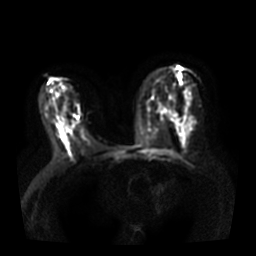
Breast MRI, one axial slice. Position 18 of 36 along the scan axis. Diffusion-weighted series; image 2 of 4 stored at this slice position (different b-values; order by instance number). 3 T. 5 mm slice thickness. 256 × 256 image matrix, field of view 360 × 360 mm. Female patient.
Outlined on this slice (expert manual segmentation):
- tumour on diffusion-weighted imaging: bounding box (x1, y1, x2, y2) in pixels: (76, 116, 79, 119)